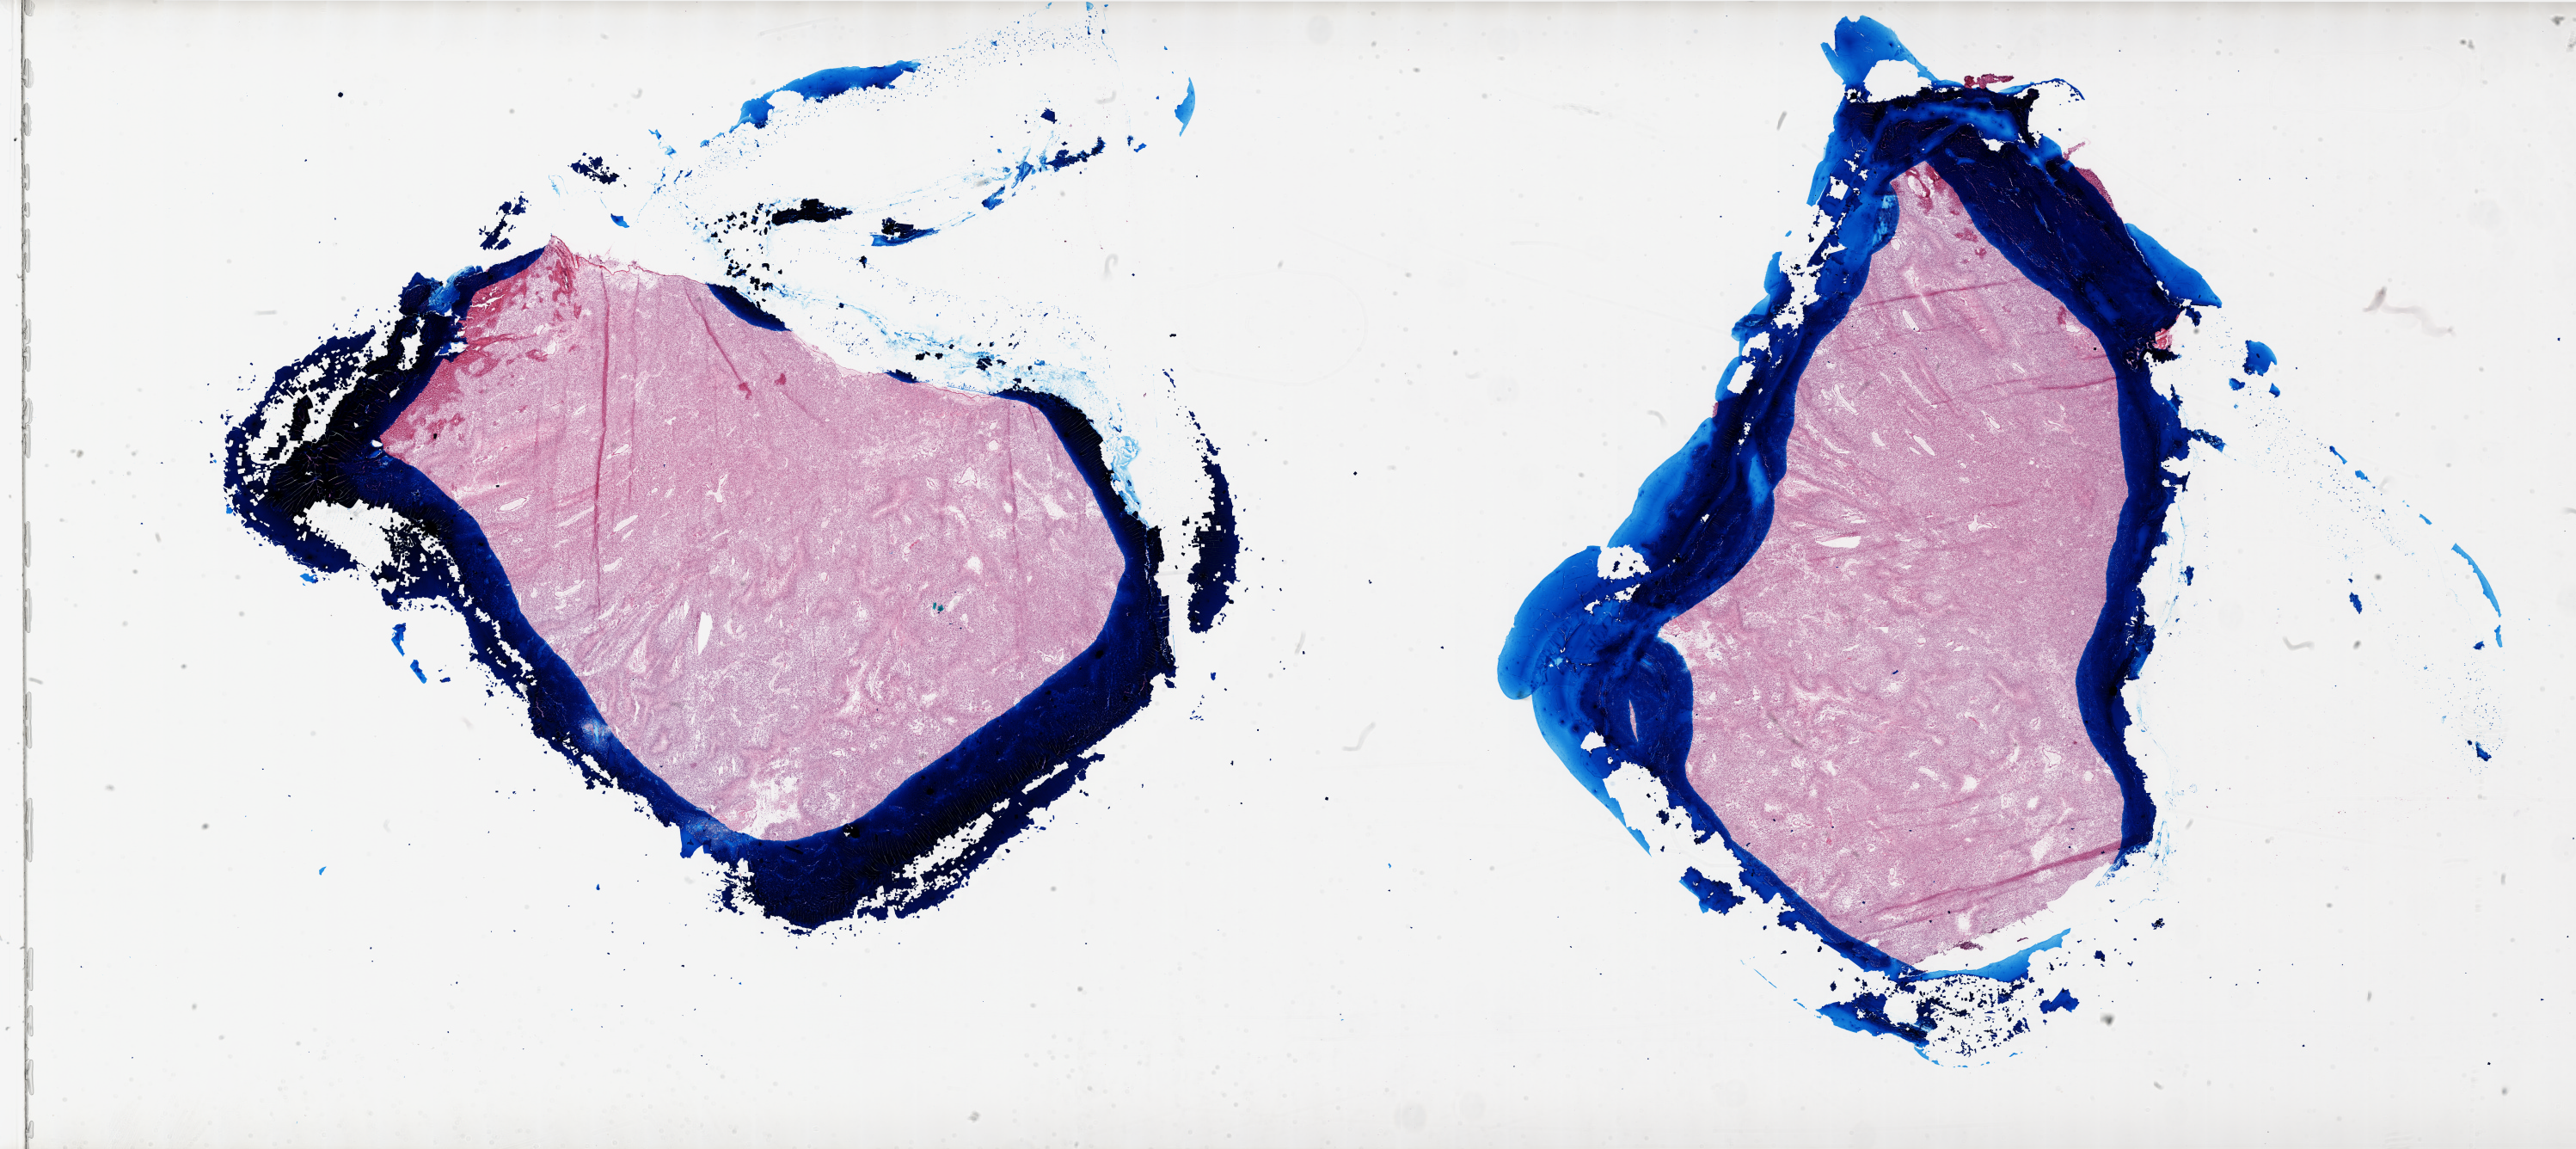
H&E whole-slide image — a low-resolution overview of the entire scanned area, about 48.0 x 21.4 mm. Frozen section from the top of the tissue portion. Sample: primary tumour, brain. Female patient; age at initial diagnosis 54 years. Composition of this section per pathologist review: tumour cells 80%, tumour nuclei 100%, normal cells 0%, stromal cells 0%, necrosis 20%.
• diagnosis: Glioblastoma